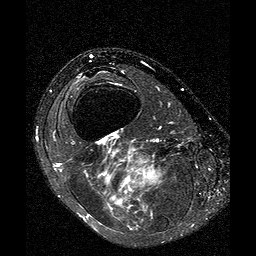
MRI of an extremity soft-tissue mass, one axial slice. Slice 24 of 25 in the series (ordered by position). T2-weighted fat-saturated. 256 × 256 image matrix, field of view 160 × 160 mm. Female patient. Case-level facts recorded for this patient, not image findings: histological type: liposarcoma; site of the primary tumour: right thigh.
Annotated regions visible in this slice (outlined manually by an expert reader):
- gross tumour volume (mass): bounding box (x1, y1, x2, y2) in pixels: (124, 167, 163, 187)